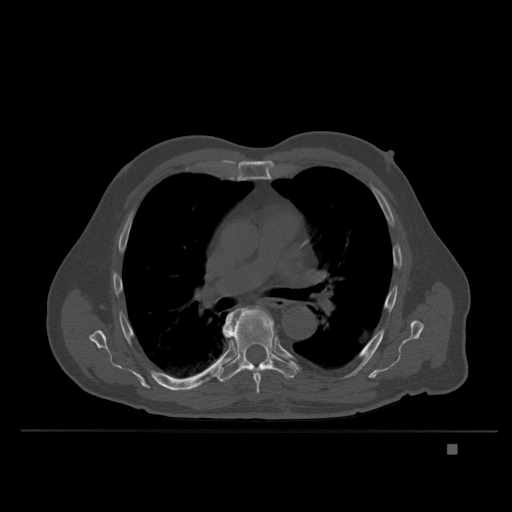
CT including the spine, one axial slice. Position 249 of 435 along the scan axis. Bone window (W 1800 / L 400 HU). 1.5 mm slice thickness. 512 × 512 image matrix. Patient: male, 73 years. Case-level facts recorded for this patient, not image findings: primary cancer: skin.
Annotated regions visible in this slice (semi-automatic segmentation, software-assisted and operator-edited):
- T6 vertebra: bounding box (x1, y1, x2, y2) in pixels: (223, 306, 263, 394)
- T7 vertebra: (216, 306, 299, 383)